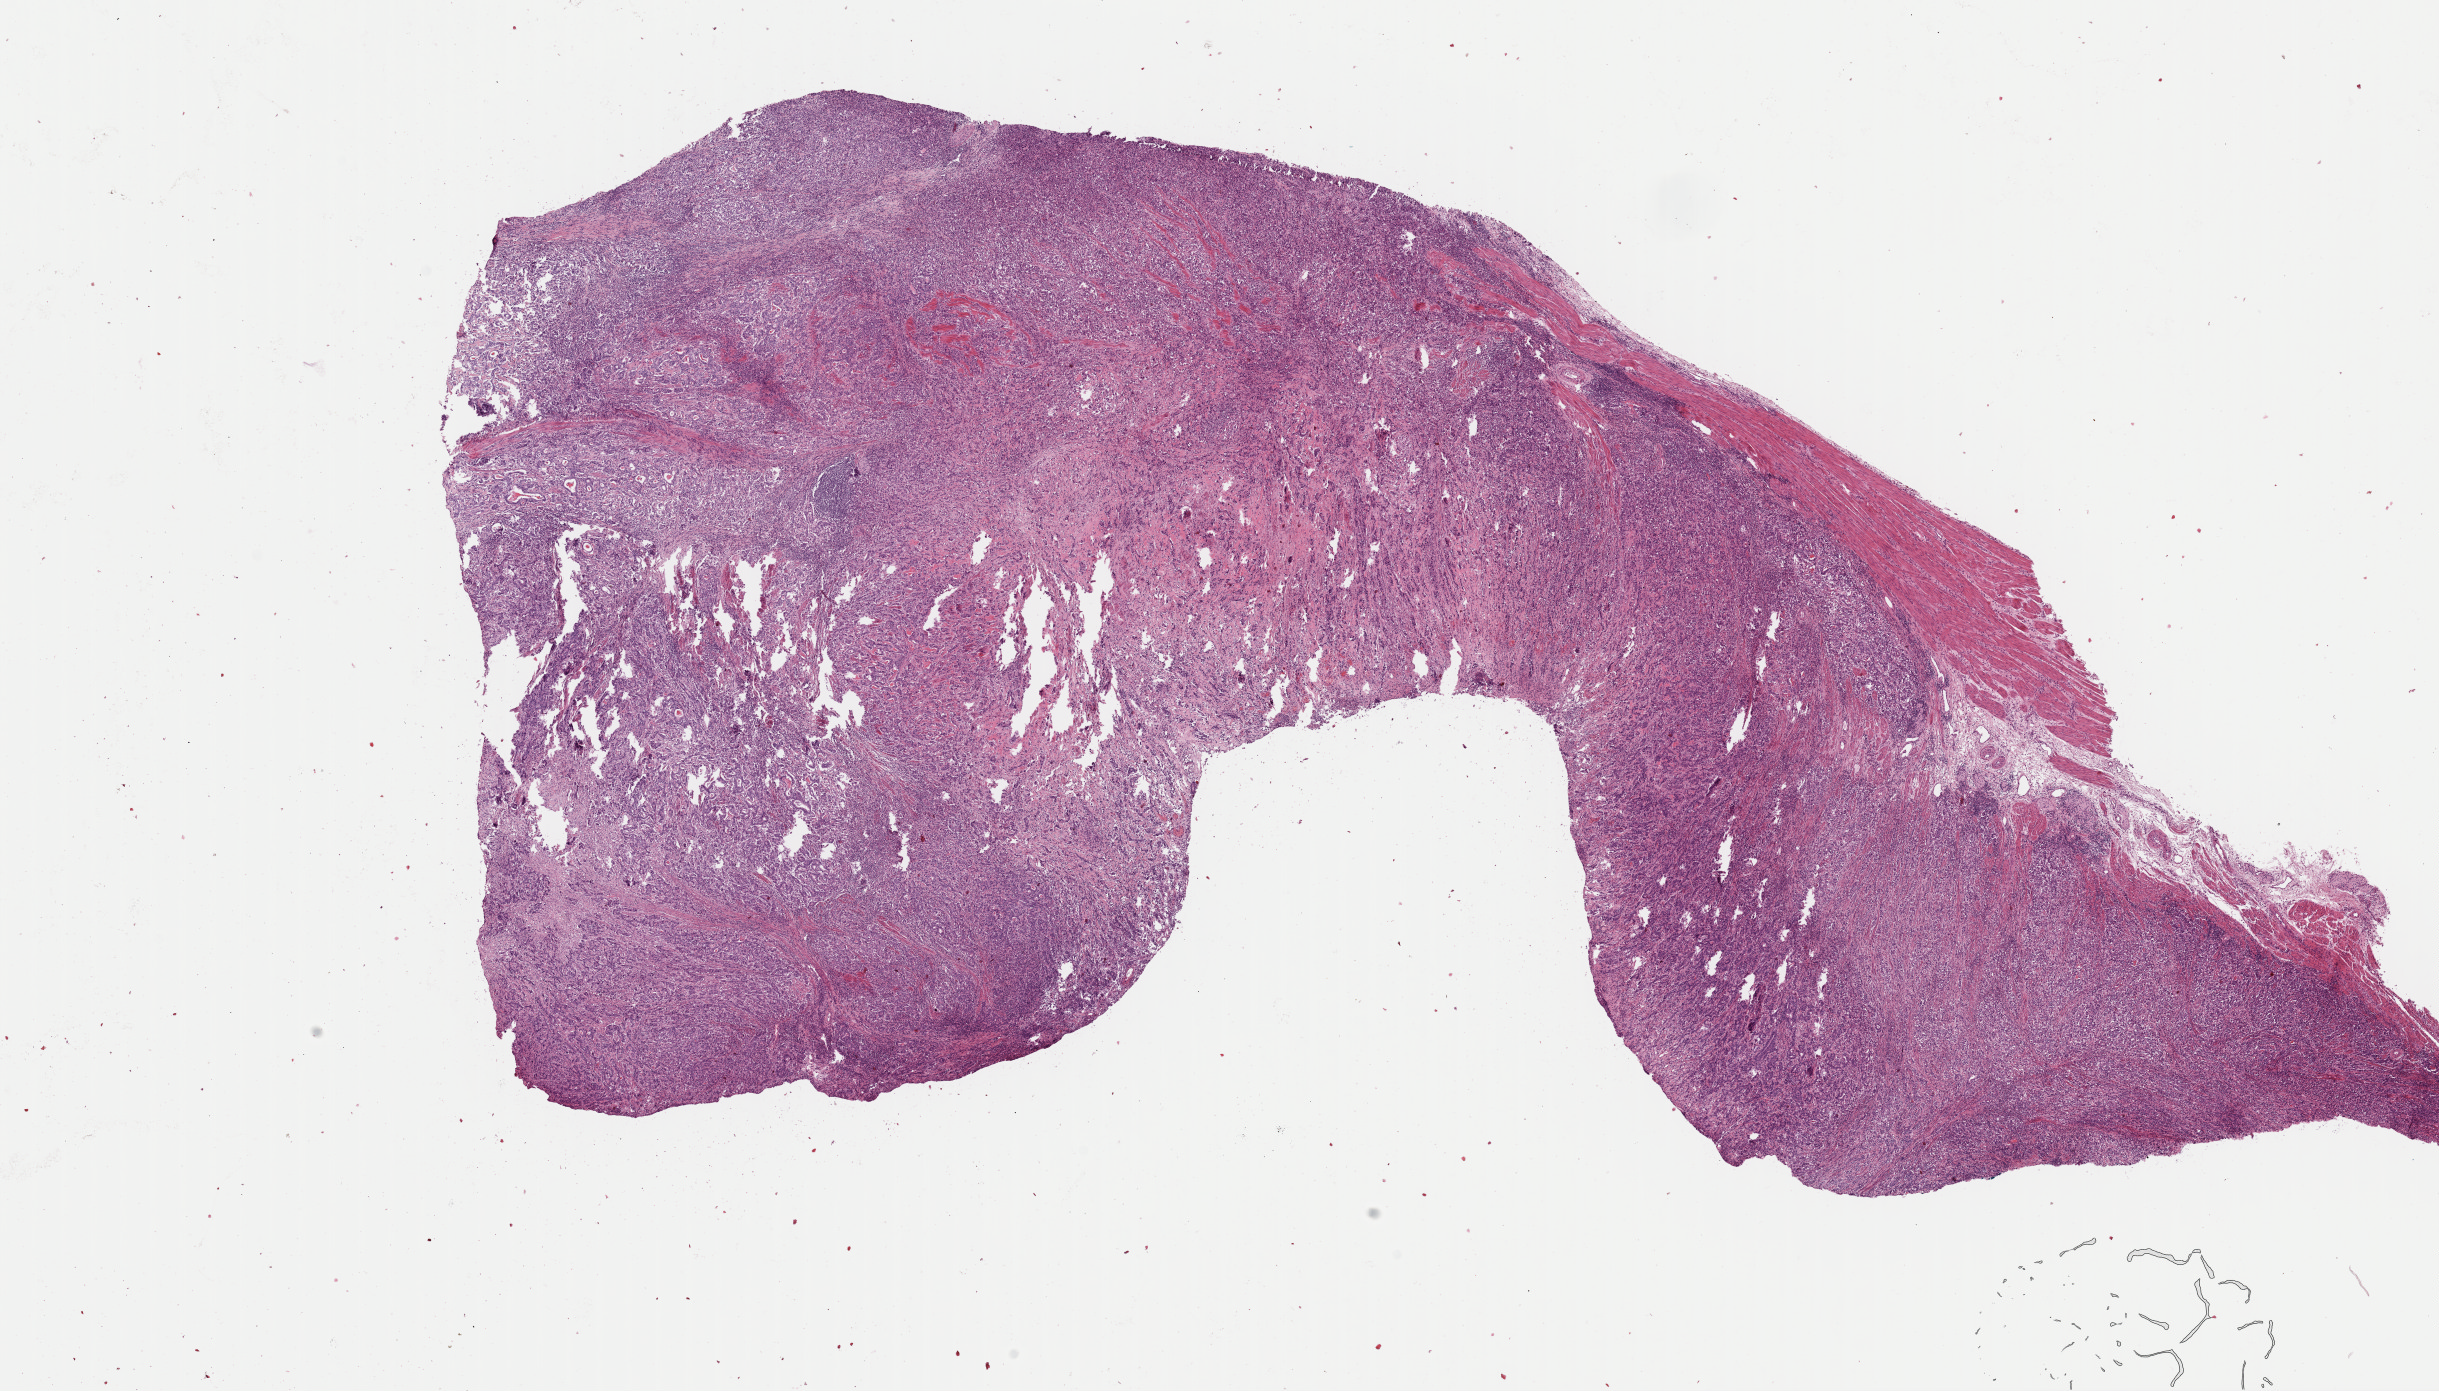
H&E whole-slide image — shown as a low-resolution overview of the whole scanned area (about 19.3 x 11.0 mm, acquisition: 40x scan); FFPE section; primary tumour sample from the stomach. Patient: male, age at initial diagnosis 44 years. Histologic grade: G3 (poorly differentiated).
• histologic diagnosis: Tubular adenocarcinoma (cardia, NOS)
• AJCC pathologic stage: IIIB (7th edition)
• TNM: T3 N3a M0